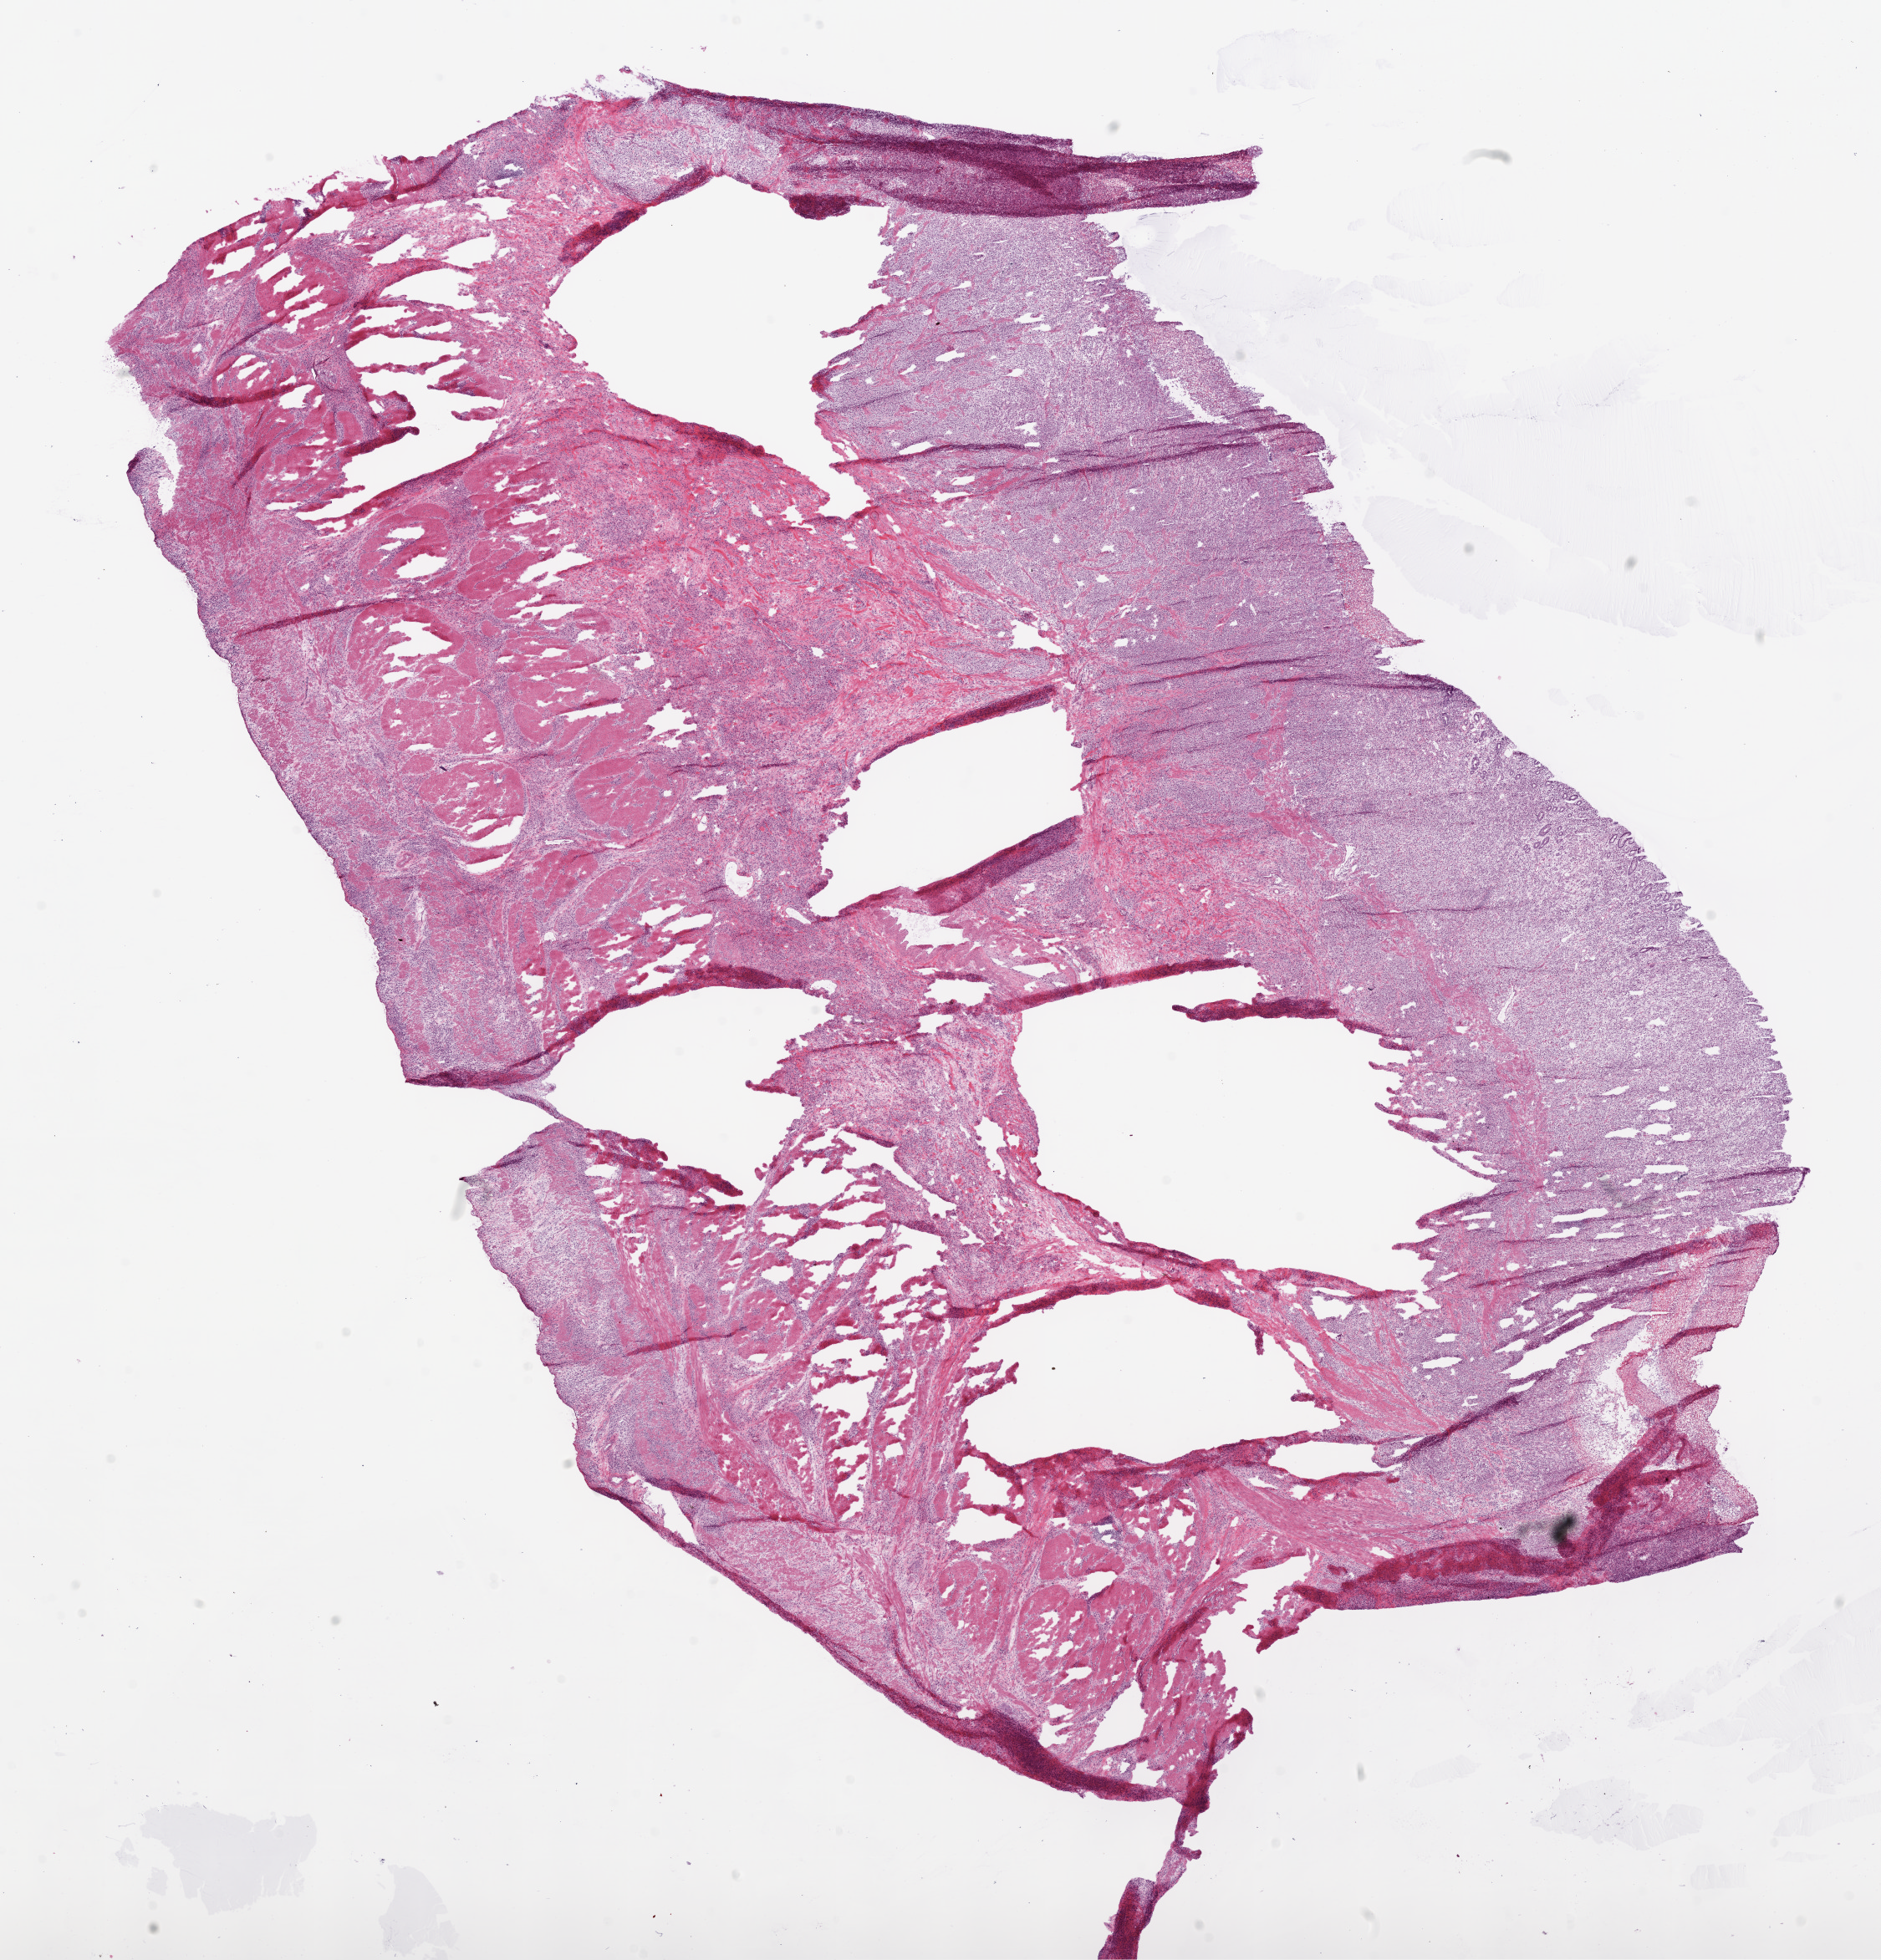
H&E whole-slide image, a low-resolution overview of the entire scanned area, about 18.1 x 18.8 mm; frozen section from the bottom of the tissue portion; primary tumour sample from the stomach. Female patient; age at initial diagnosis 53 years. Histologic grade: G3 (poorly differentiated). Pathologist review of this section (percent, as recorded): tumour cells 75%, tumour nuclei 80%, normal cells 15%, stromal cells 10%, necrosis 0%.
- histologic diagnosis: Adenocarcinoma, NOS (cardia, NOS)
- lymph nodes positive (case pathology): 2 of 8 examined